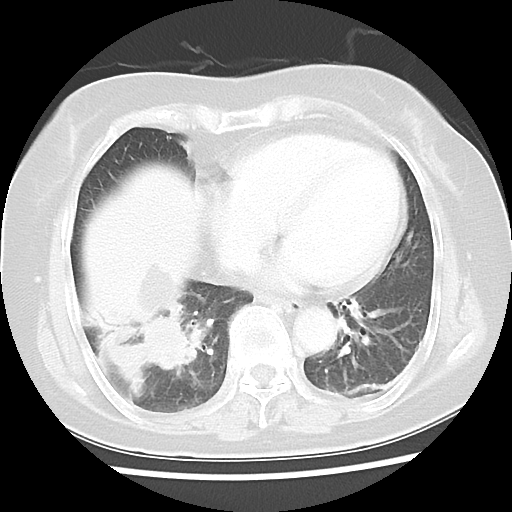
Chest CT, one axial slice. Slice 15 of 45 in the series (ordered by position). 120 kVp. Lung window (W 1500 / L -600 HU). 5 mm slice thickness. 512 × 512 image matrix, field of view 312 × 312 mm. Patient: female, 65 years. From the clinical record (not read from this slice): clinical TNM (as recorded): T2 N3 M0.
Structures marked on this image (rectangle marked by the reading radiologist):
- lung tumour (recorded histology: adenocarcinoma): box from (x=134, y=311) to (x=204, y=386) px